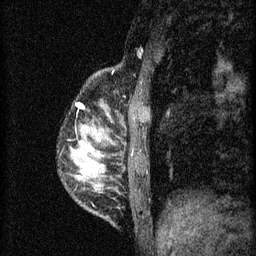
Breast MRI (dynamic contrast-enhanced), one sagittal slice. Slice 10 of 60 in the series (ordered by position). 3 images stored at this slice position (order not interpretable as contrast timing). 1.5 T. TE 4.2 ms, TR 8.2 ms. 256 × 256 image matrix, field of view 180 × 180 mm. Patient: female, 37 years.
Structures marked on this image (semi-automatically segmented with operator editing):
- analysis volume of interest (the breast-tissue region the enhancement analysis was run in; not a lesion): box from (x=70, y=102) to (x=140, y=181) px
- tumour enhancement mask (voxels above the 70 % enhancement threshold inside the analysis volume of interest): (x=80, y=104)–(x=83, y=107)